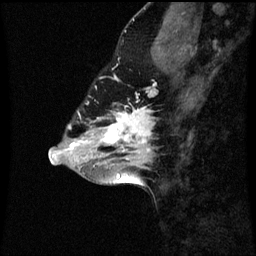
Breast MRI (dynamic contrast-enhanced), one sagittal slice; slice 25 of 60 in the series (ordered by position); dynamic contrast-enhanced series, image 2 of 3 at this slice position (ordered by acquisition); 1.5 T; TE 4.2 ms, TR 8.9 ms; 2 mm slice thickness; 256 × 256 image matrix. Patient: female, 43 years. Case-level facts recorded for this patient, not image findings: setting: breast cancer imaged before/during neoadjuvant chemotherapy; receptor status: HR-positive, HER2-negative.
Structures marked on this image (semi-automatic segmentation, software-assisted and operator-edited):
- analysis volume of interest (the breast-tissue region the enhancement analysis was run in; not a lesion): bounding box [x1, y1, x2, y2] px = [96, 96, 159, 159]
- tumour enhancement mask (voxels above the 70 % enhancement threshold inside the analysis volume of interest): [104, 96, 153, 151]